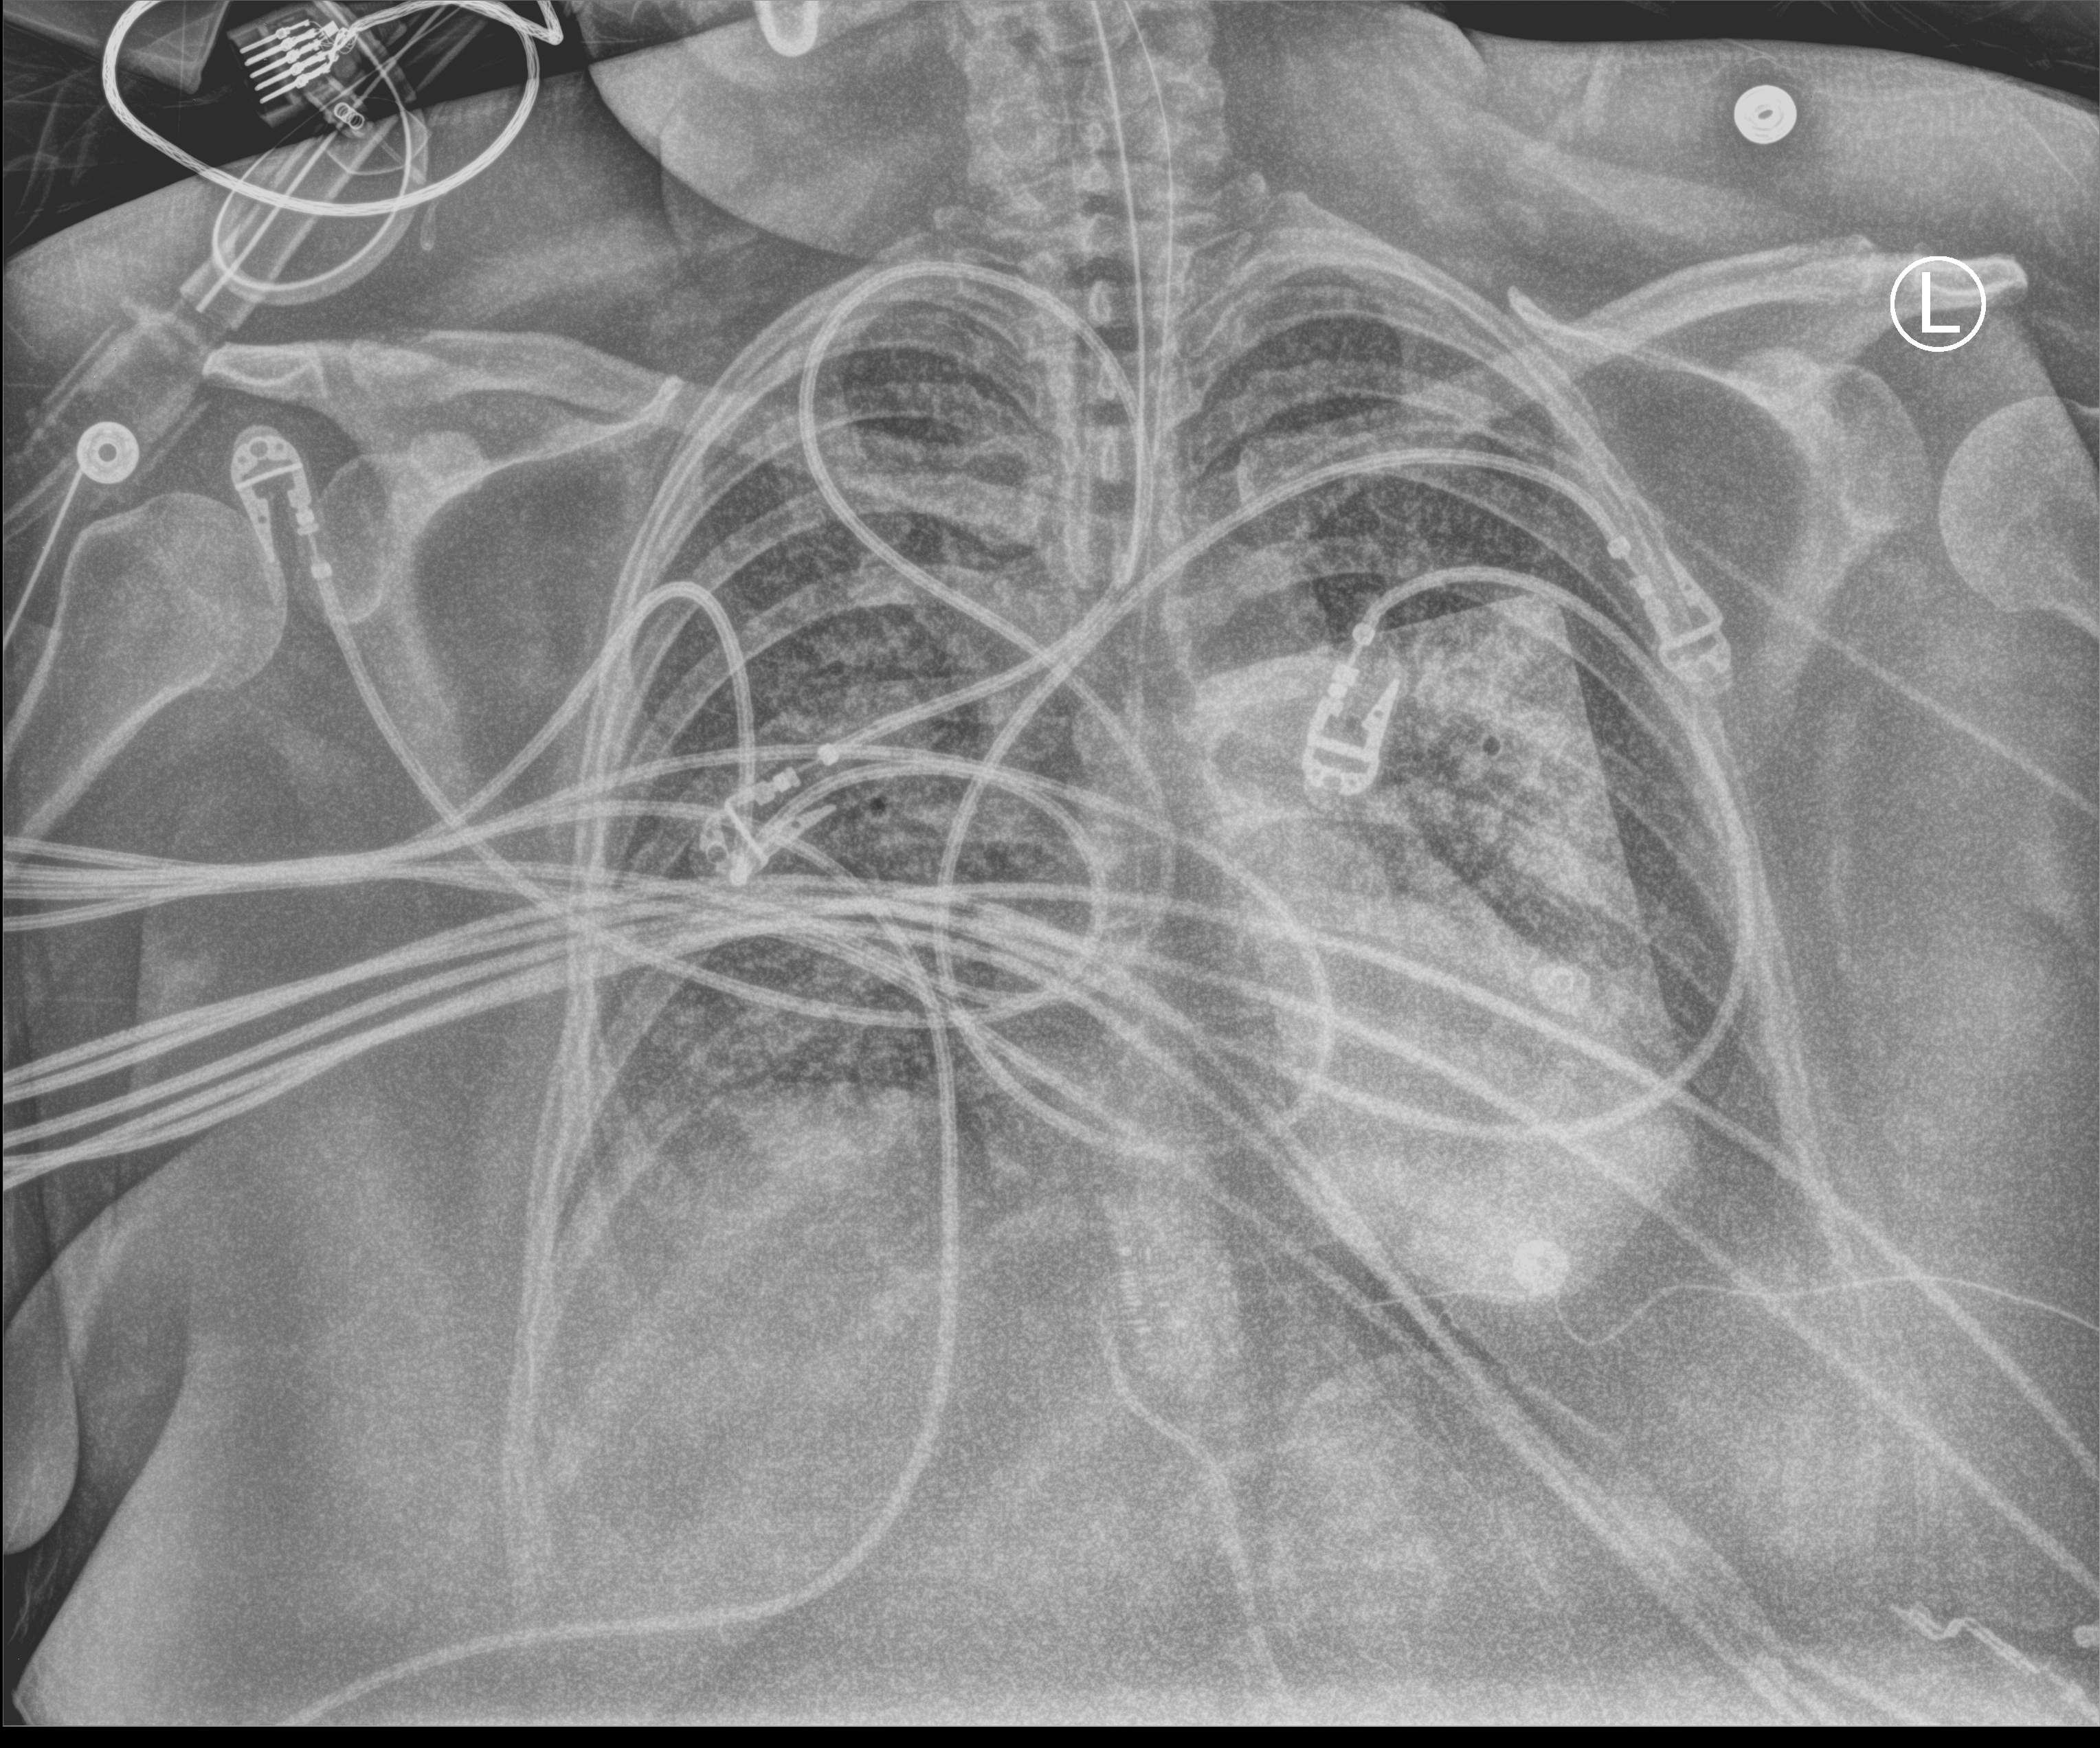
Bedside chest radiograph (computed radiography), anteroposterior (AP) projection. Female patient hospitalised with COVID-19, age 18–59 years.
Hospital-stay facts (about this admission, not read from this image; timing relative to this image not recorded): chronic kidney disease (admission record): no.